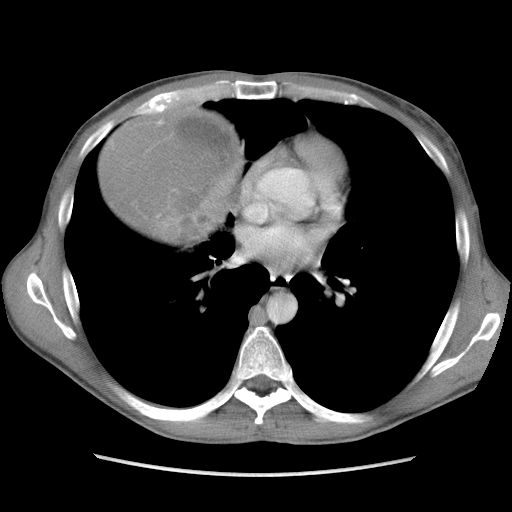
Contrast-enhanced abdominal CT, one axial slice. Slice 103 of 115 in the series (ordered by position). Soft-tissue window (W 400 / L 40 HU). 5 mm slice thickness. 512 × 512 image matrix, field of view 360 × 360 mm. Male patient. From the clinical record (not read from this slice): diagnosis: adrenocortical carcinoma; tumour side: right adrenal.
Outlined on this slice (semi-automatically segmented with operator editing):
- mass: bounding box <105,111,237,240> (left, top, right, bottom; pixels)